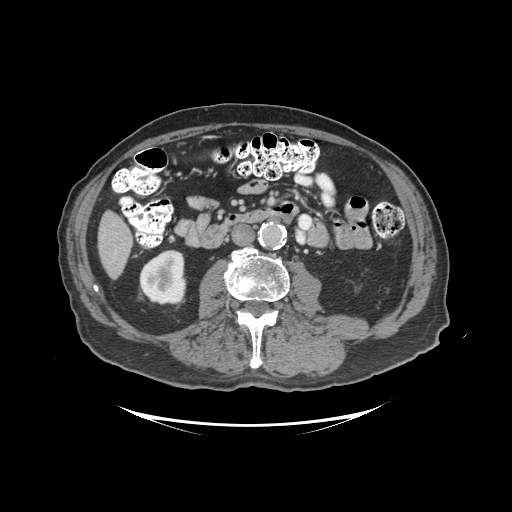
Contrast-enhanced abdominal CT (liver protocol), one axial slice; position 28 of 99 along the scan axis; reconstruction kernel STANDARD; 140 kVp; soft-tissue window (W 400 / L 40 HU); 2.5 mm slice thickness; 512 × 512 image matrix, field of view 460 × 460 mm. Case-level facts recorded for this patient, not image findings: diagnosis: hepatocellular carcinoma (patient treated with transarterial chemoembolisation; whether this scan precedes or follows treatment is not stated here); TNM stage (as recorded): Stage-I; Child-Pugh class: A; tumour differentiation: moderately differentiated; tumour nodularity: uninodular.
Outlined on this slice (semi-automatically segmented with operator editing):
- liver parenchyma outside the tumour (the mass and vessels are separate outlines, so this box may not span the whole liver): bounding box (x1, y1, x2, y2) in pixels: (98, 210, 132, 278)